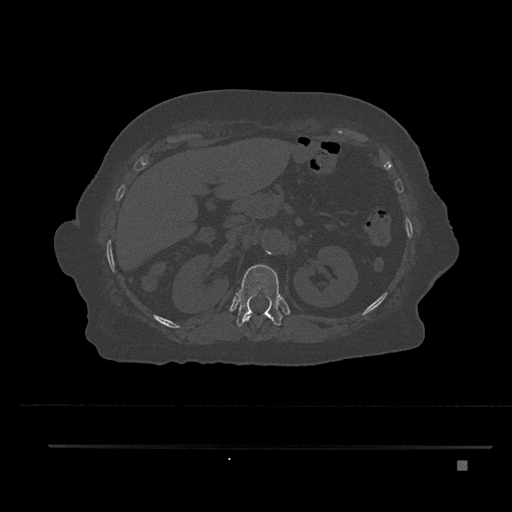
CT including the spine, one axial slice; slice 272 of 797 in the series (ordered by position); reconstruction kernel Br40s/3; 120 kVp; bone window (W 1800 / L 400 HU); 0.5 mm slice thickness; 512 × 512 image matrix, field of view 437 × 437 mm. Female patient, age 76 years. From the clinical record (not read from this slice): primary cancer: lung; vertebrae with lytic lesions (as recorded): T11, L3.
Annotated regions visible in this slice (semi-automatic segmentation, software-assisted and operator-edited):
- T11 vertebra: bounding box [x1, y1, x2, y2] px = [243, 313, 261, 340]
- T12 vertebra: [236, 265, 282, 327]